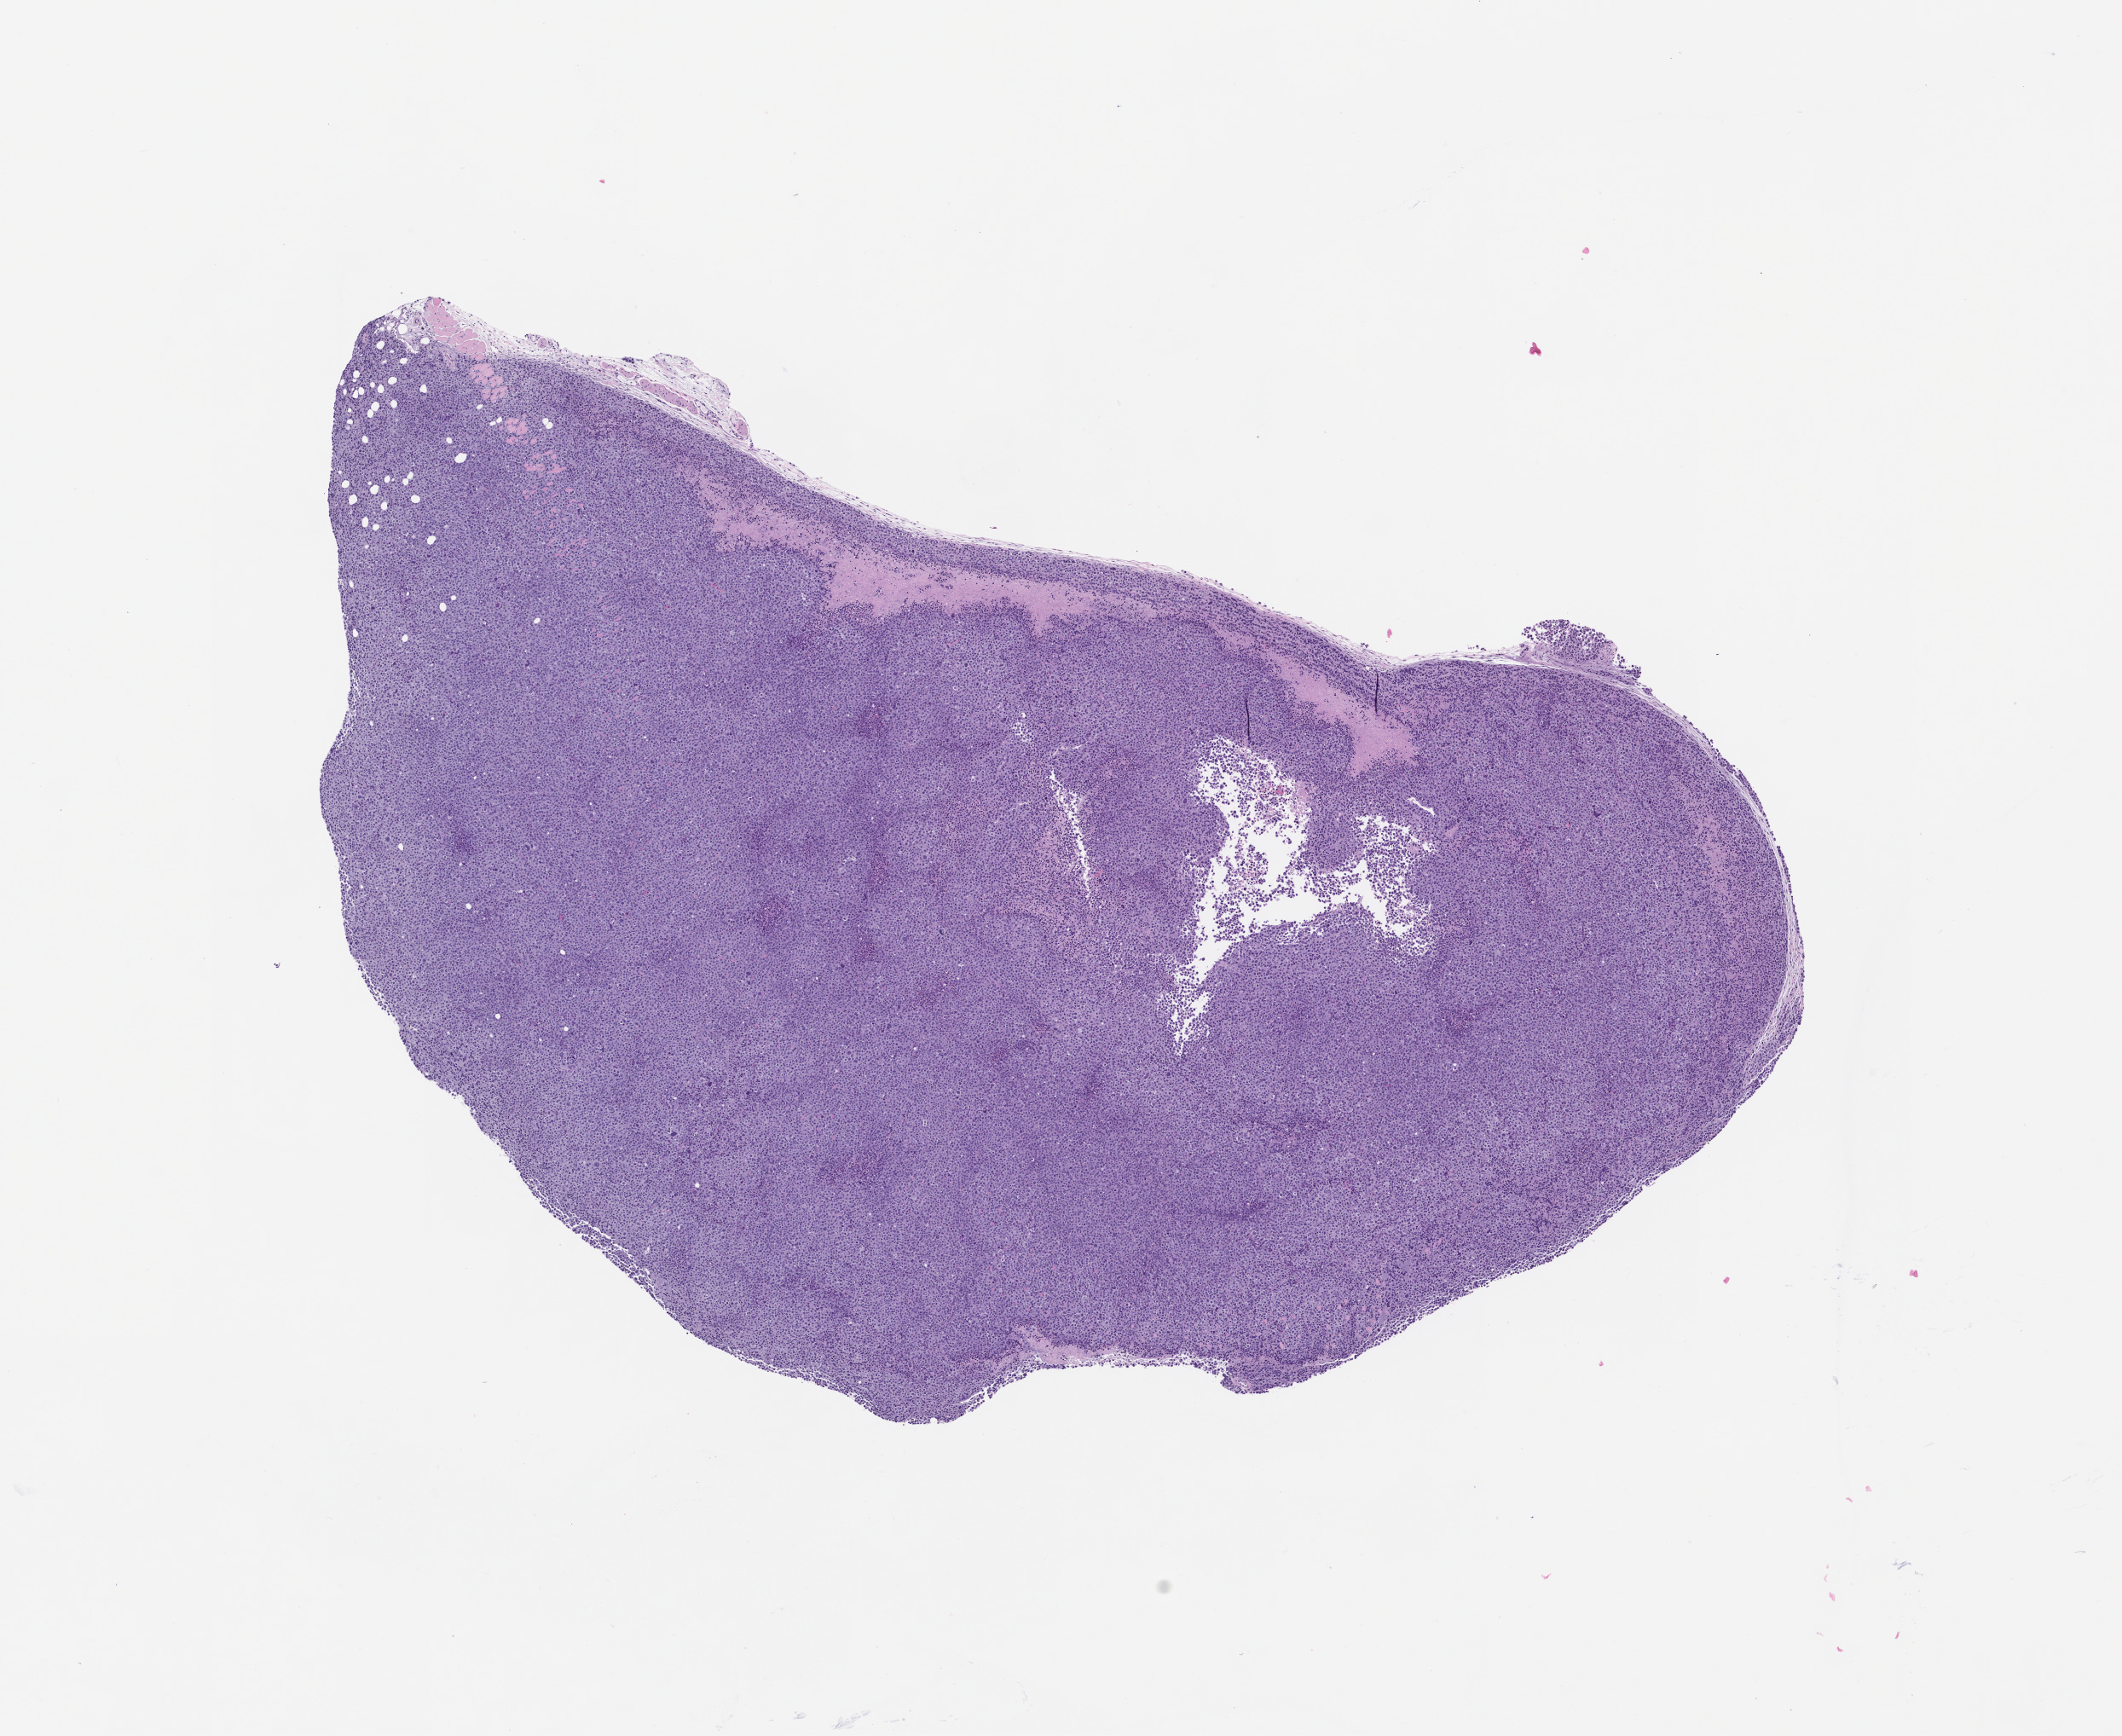
Haematoxylin and eosin whole-slide image of a patient-derived xenograft (PDX) tumor grown in a mouse, passage 5 — shown as a low-resolution overview of the whole scanned area (about 10.0 x 8.2 mm). FFPE section. Tumor site category: bladder.
• originating patient diagnosis: Urothelial Carcinoma